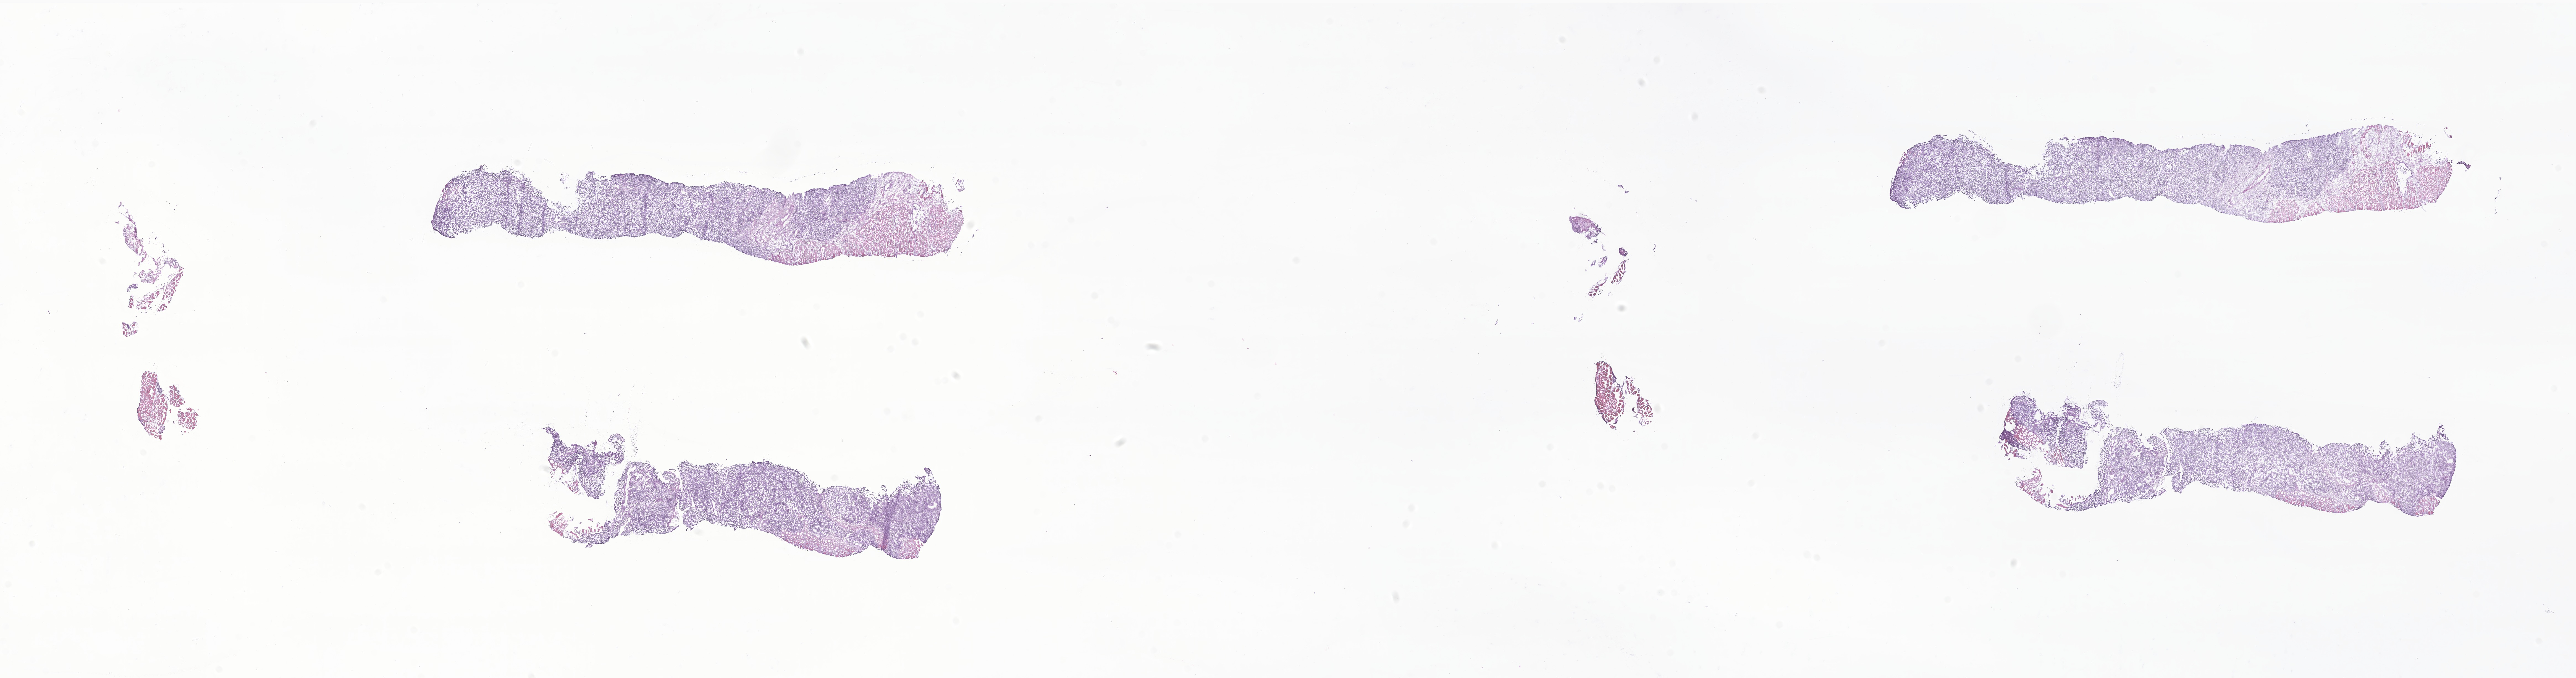
H&E whole-slide image of tumor tissue from the soft tissue of upper extremity, low-resolution overview of the scanned area, about 39.3 x 10.3 mm; cryosection (OCT / tissue freezing medium). Patient male; age 135 months (11 years 3 months).
Tissue or organ of origin (case record): connective, subcutaneous and other soft tissues of upper limb and shoulder. Diagnosis: Alveolar rhabdomyosarcoma.